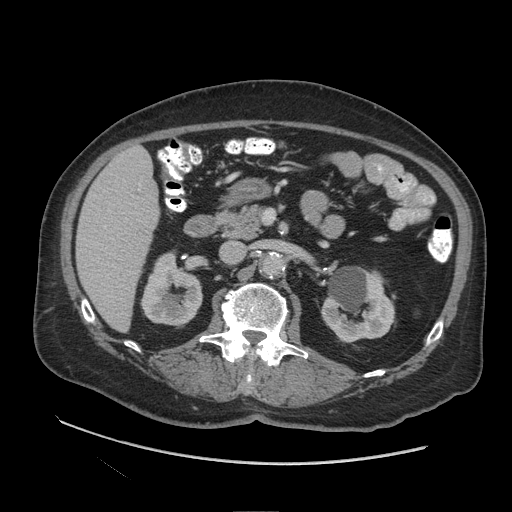
Contrast-enhanced abdominal CT (liver protocol), one axial slice; reconstruction kernel STANDARD; soft-tissue window (W 400 / L 40 HU); 2.5 mm slice thickness; 512 × 512 image matrix, field of view 420 × 420 mm. From the clinical record (not read from this slice): diagnosis: hepatocellular carcinoma (patient treated with transarterial chemoembolisation; whether this scan precedes or follows treatment is not stated here); TNM stage (as recorded): Stage-I; Child-Pugh class: A; tumour nodularity: uninodular.
Outlined on this slice (semi-automatically segmented with operator editing):
- liver parenchyma outside the tumour (the mass and vessels are separate outlines, so this box may not span the whole liver): bounding box <76,146,160,330> (left, top, right, bottom; pixels)
- liver vessels: <105,184,141,267>